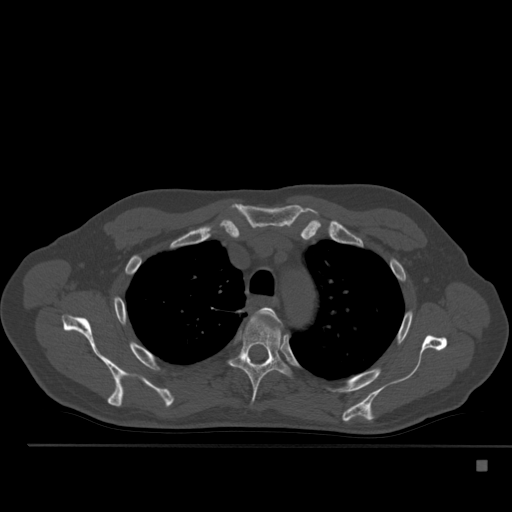
CT including the spine, one axial slice. Slice 383 of 517 in the series (ordered by position). Reconstruction kernel Br40s. Bone window (W 1800 / L 400 HU). 1.5 mm slice thickness. 512 × 512 image matrix, field of view 408 × 408 mm. Patient: male, 70 years. Case-level facts recorded for this patient, not image findings: primary cancer: renal; vertebrae with lytic lesions (as recorded): T4, T6, T10, T12, L3, L4, L5.
Outlined on this slice (semi-automatic segmentation, software-assisted and operator-edited):
- T3 vertebra: bounding box <260,307,279,321> (left, top, right, bottom; pixels)
- T4 vertebra: <229,314,289,405>